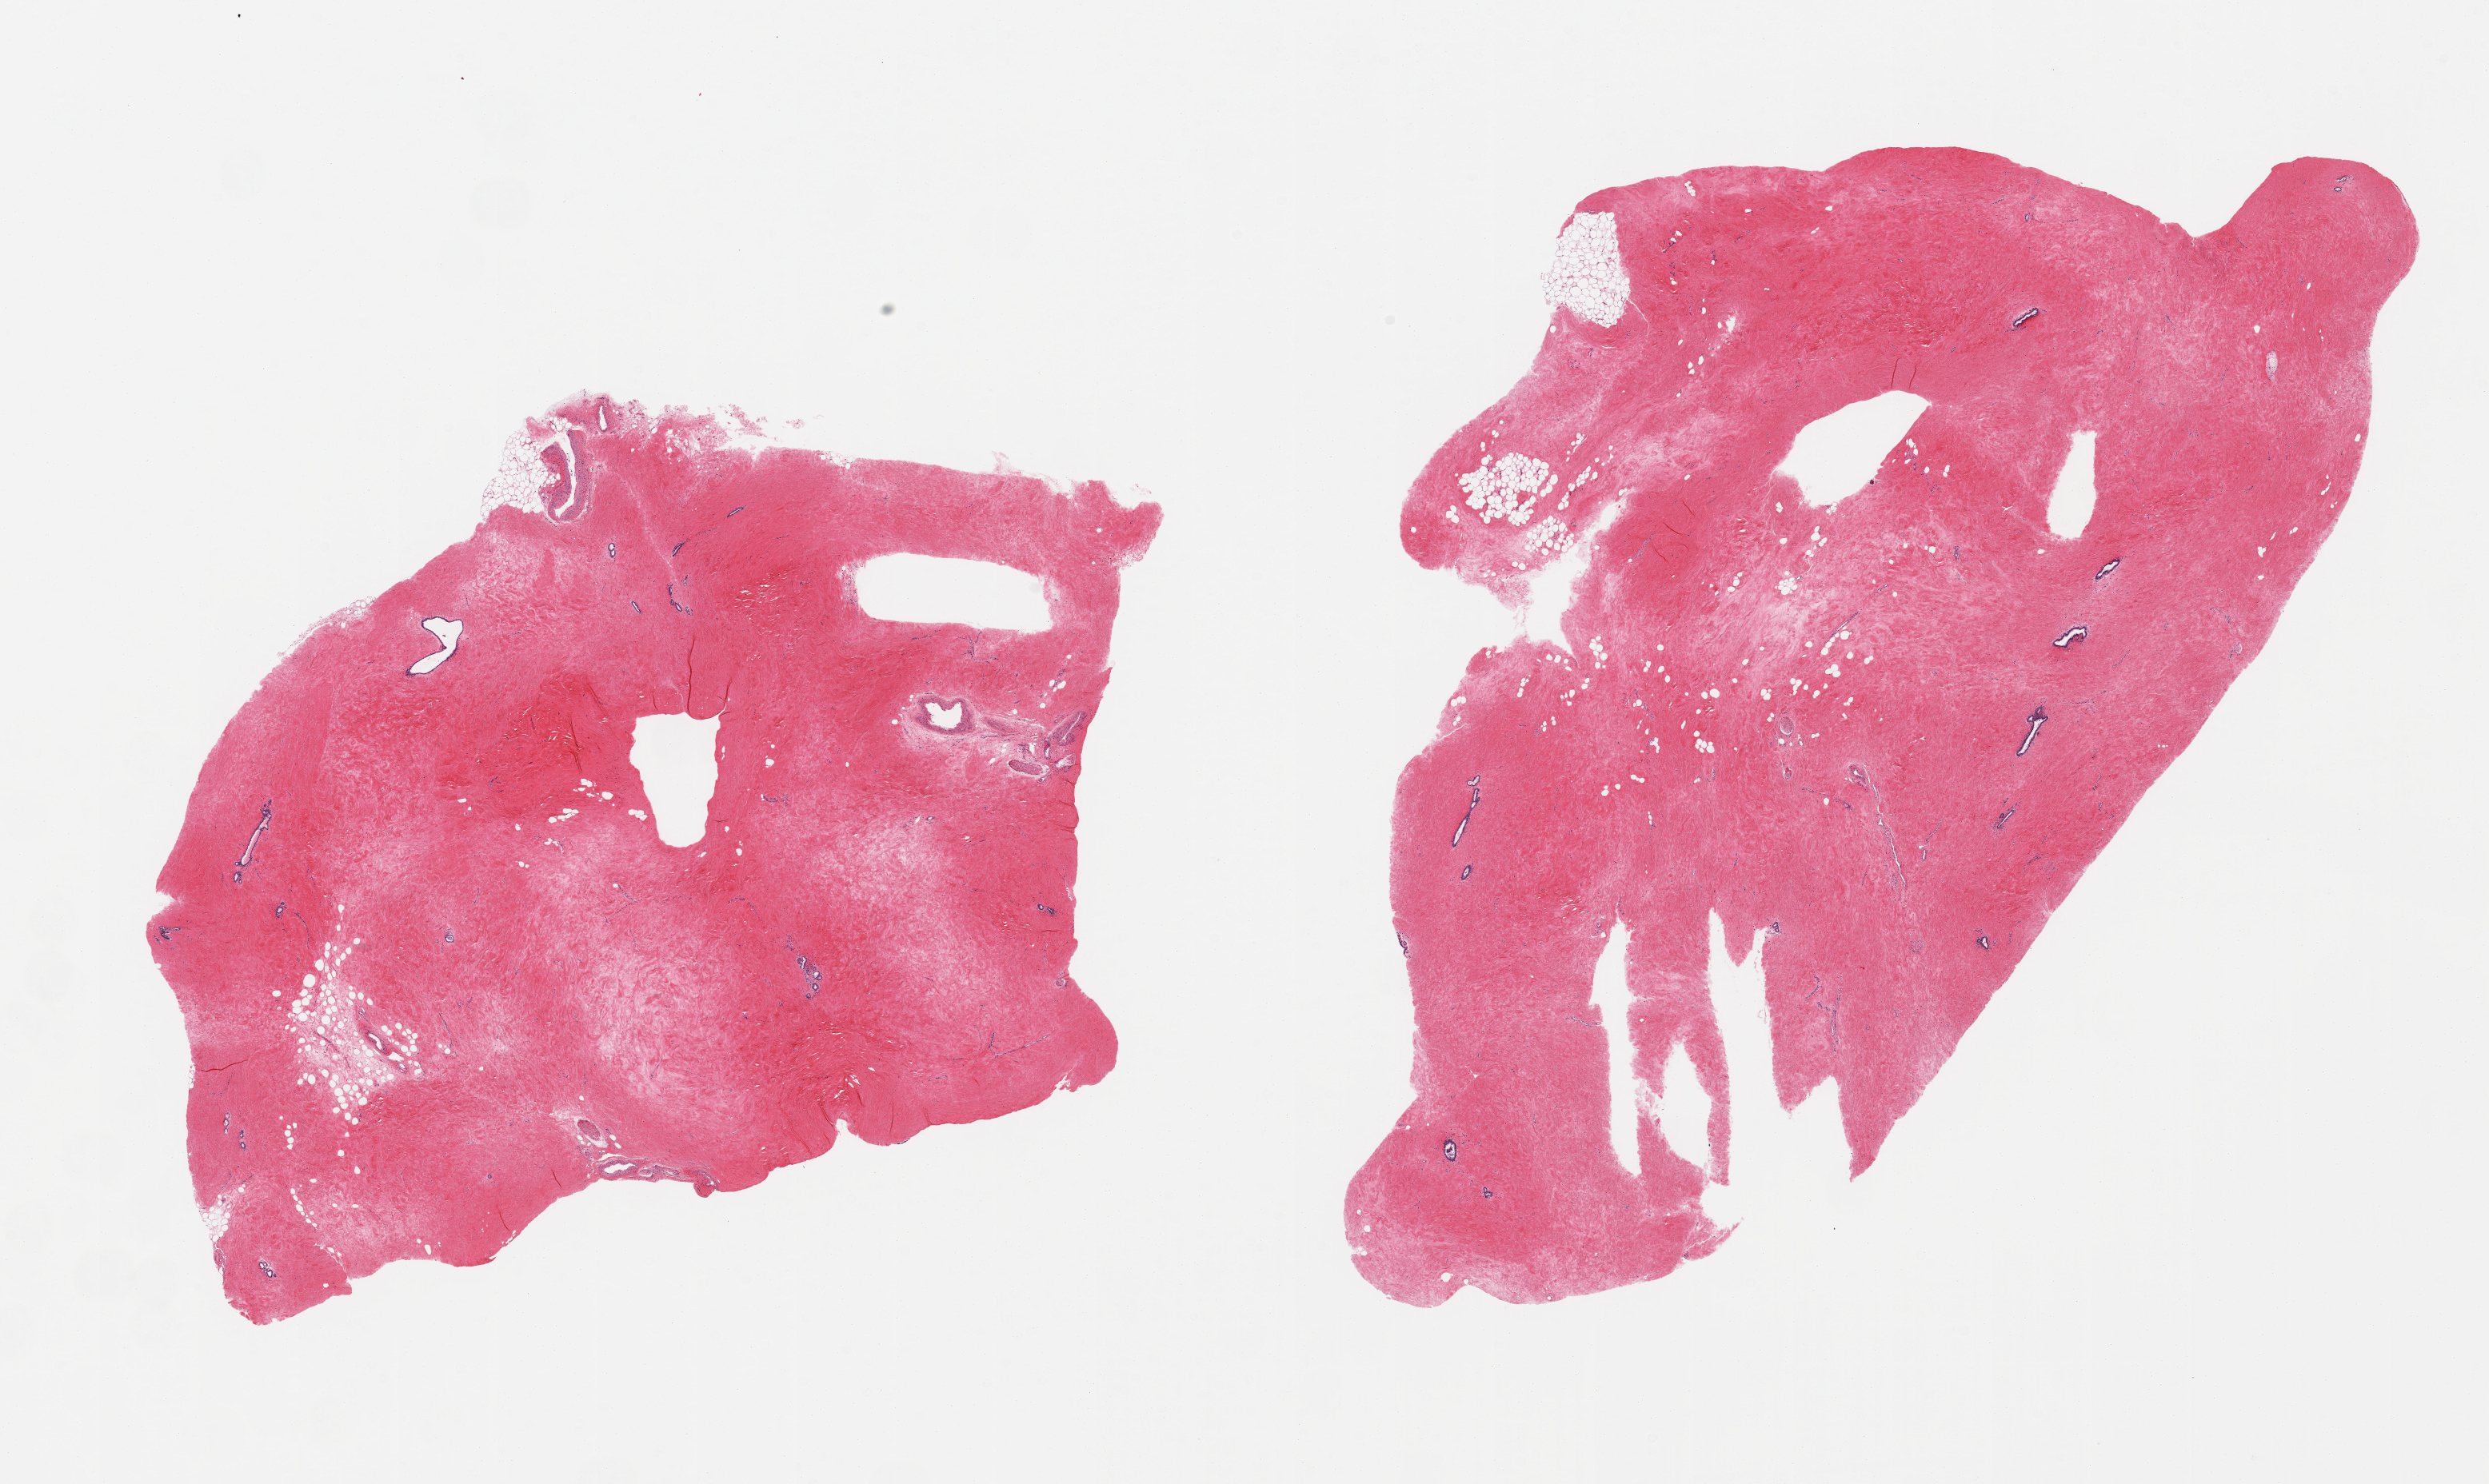
Whole-slide image, haematoxylin and eosin stain, whole scanned area (about 24.6 x 14.7 mm) shown as a low-resolution overview. PAXgene-fixed paraffin-embedded (PFPE) section. Sampled site (target tissue): breast. Donor tissue sample. Donor sex: male.
Reviewer comment on this tissue sample: 2 pieces, gynecomastoid stromal hyerplasia, rare ductal elements noted.